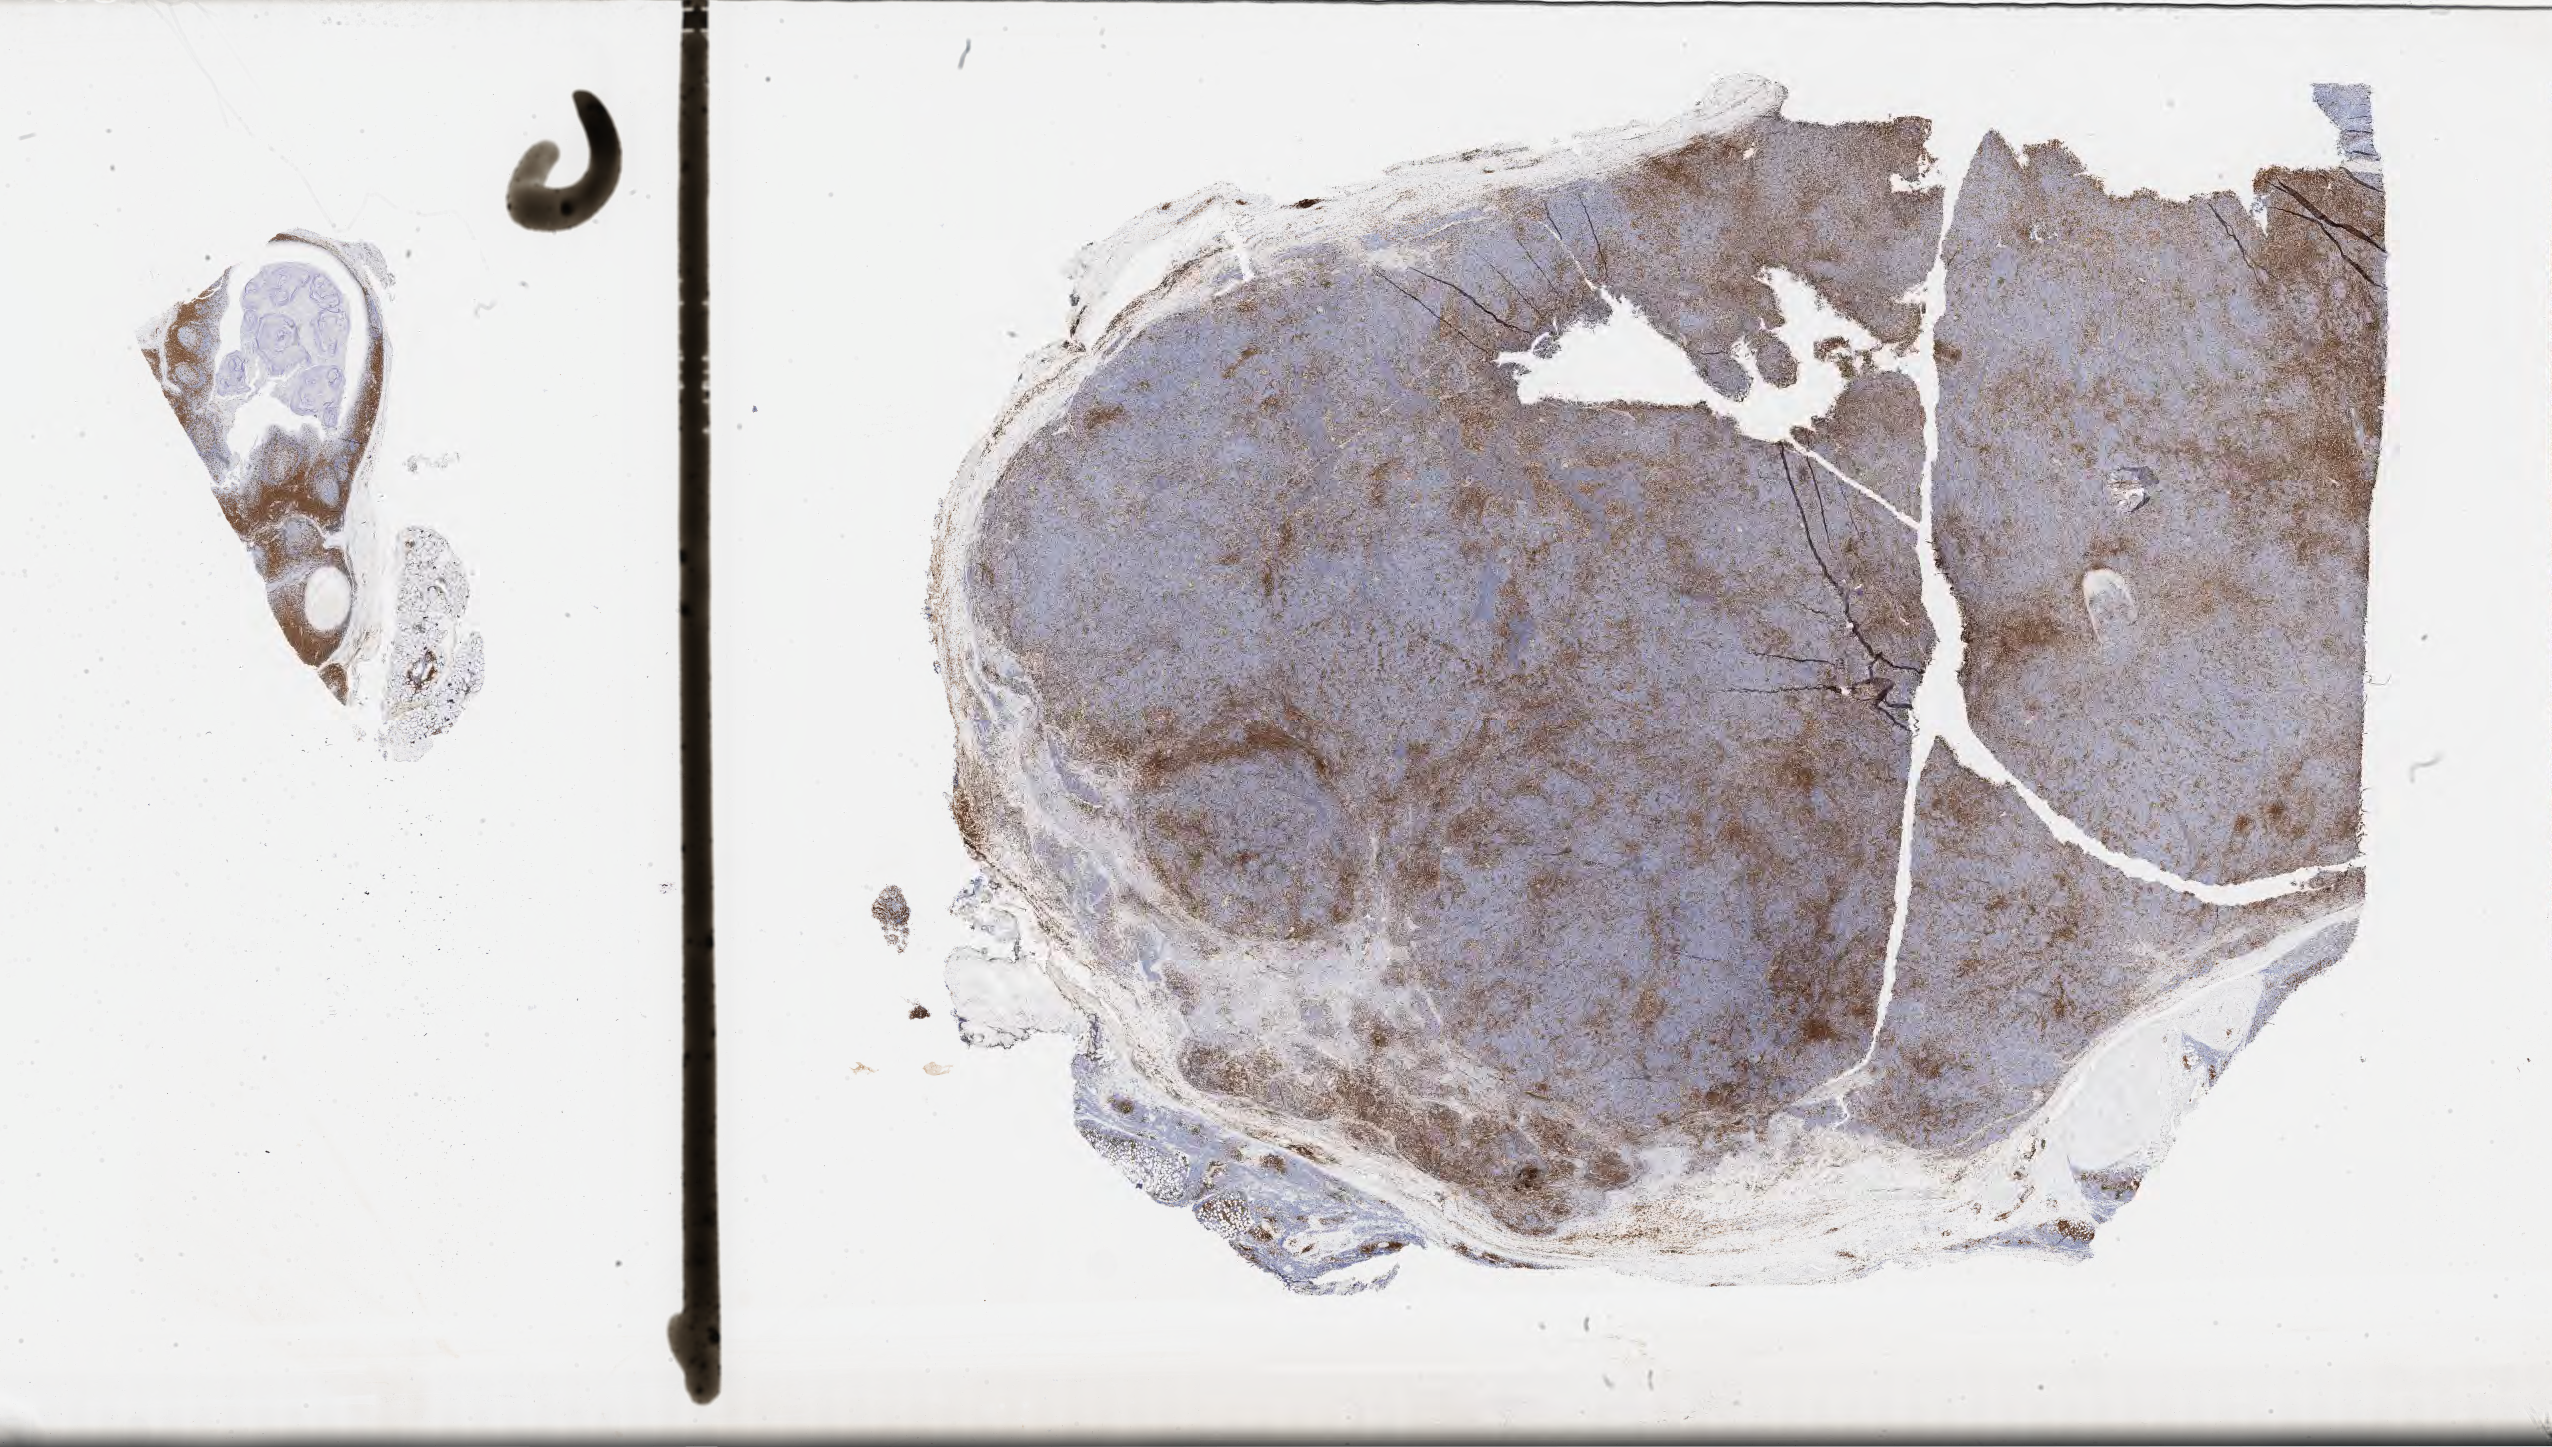
IHC for CD3, whole-slide image, shown as a low-resolution overview of the whole scanned area (about 41.3 x 23.4 mm). Tumor tissue. Patient: male, age 30 years.
* histologic diagnosis: Burkitt lymphoma, NOS